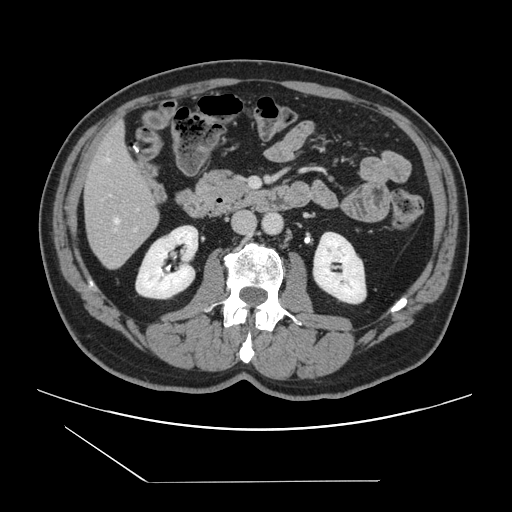
Contrast-enhanced abdominal CT, one axial slice; intravenous contrast given; soft-tissue window (W 400 / L 40 HU); 2.5 mm slice thickness; 512 × 512 image matrix, field of view 407 × 407 mm. Male patient, age 61 years. Case-level facts recorded for this patient, not image findings: diagnosis: colorectal cancer liver metastases, imaged before liver resection; multiple liver metastases: yes; largest metastasis: 5.5 cm.
Structures marked on this image (manually delineated by an expert):
- hepatic veins: bounding box <107,158,119,229> (left, top, right, bottom; pixels)
- liver: <85,126,159,268>
- planned liver remnant (the part of the liver to remain after resection): <85,127,155,218>
- portal vein (with intrahepatic branches): <110,194,137,230>